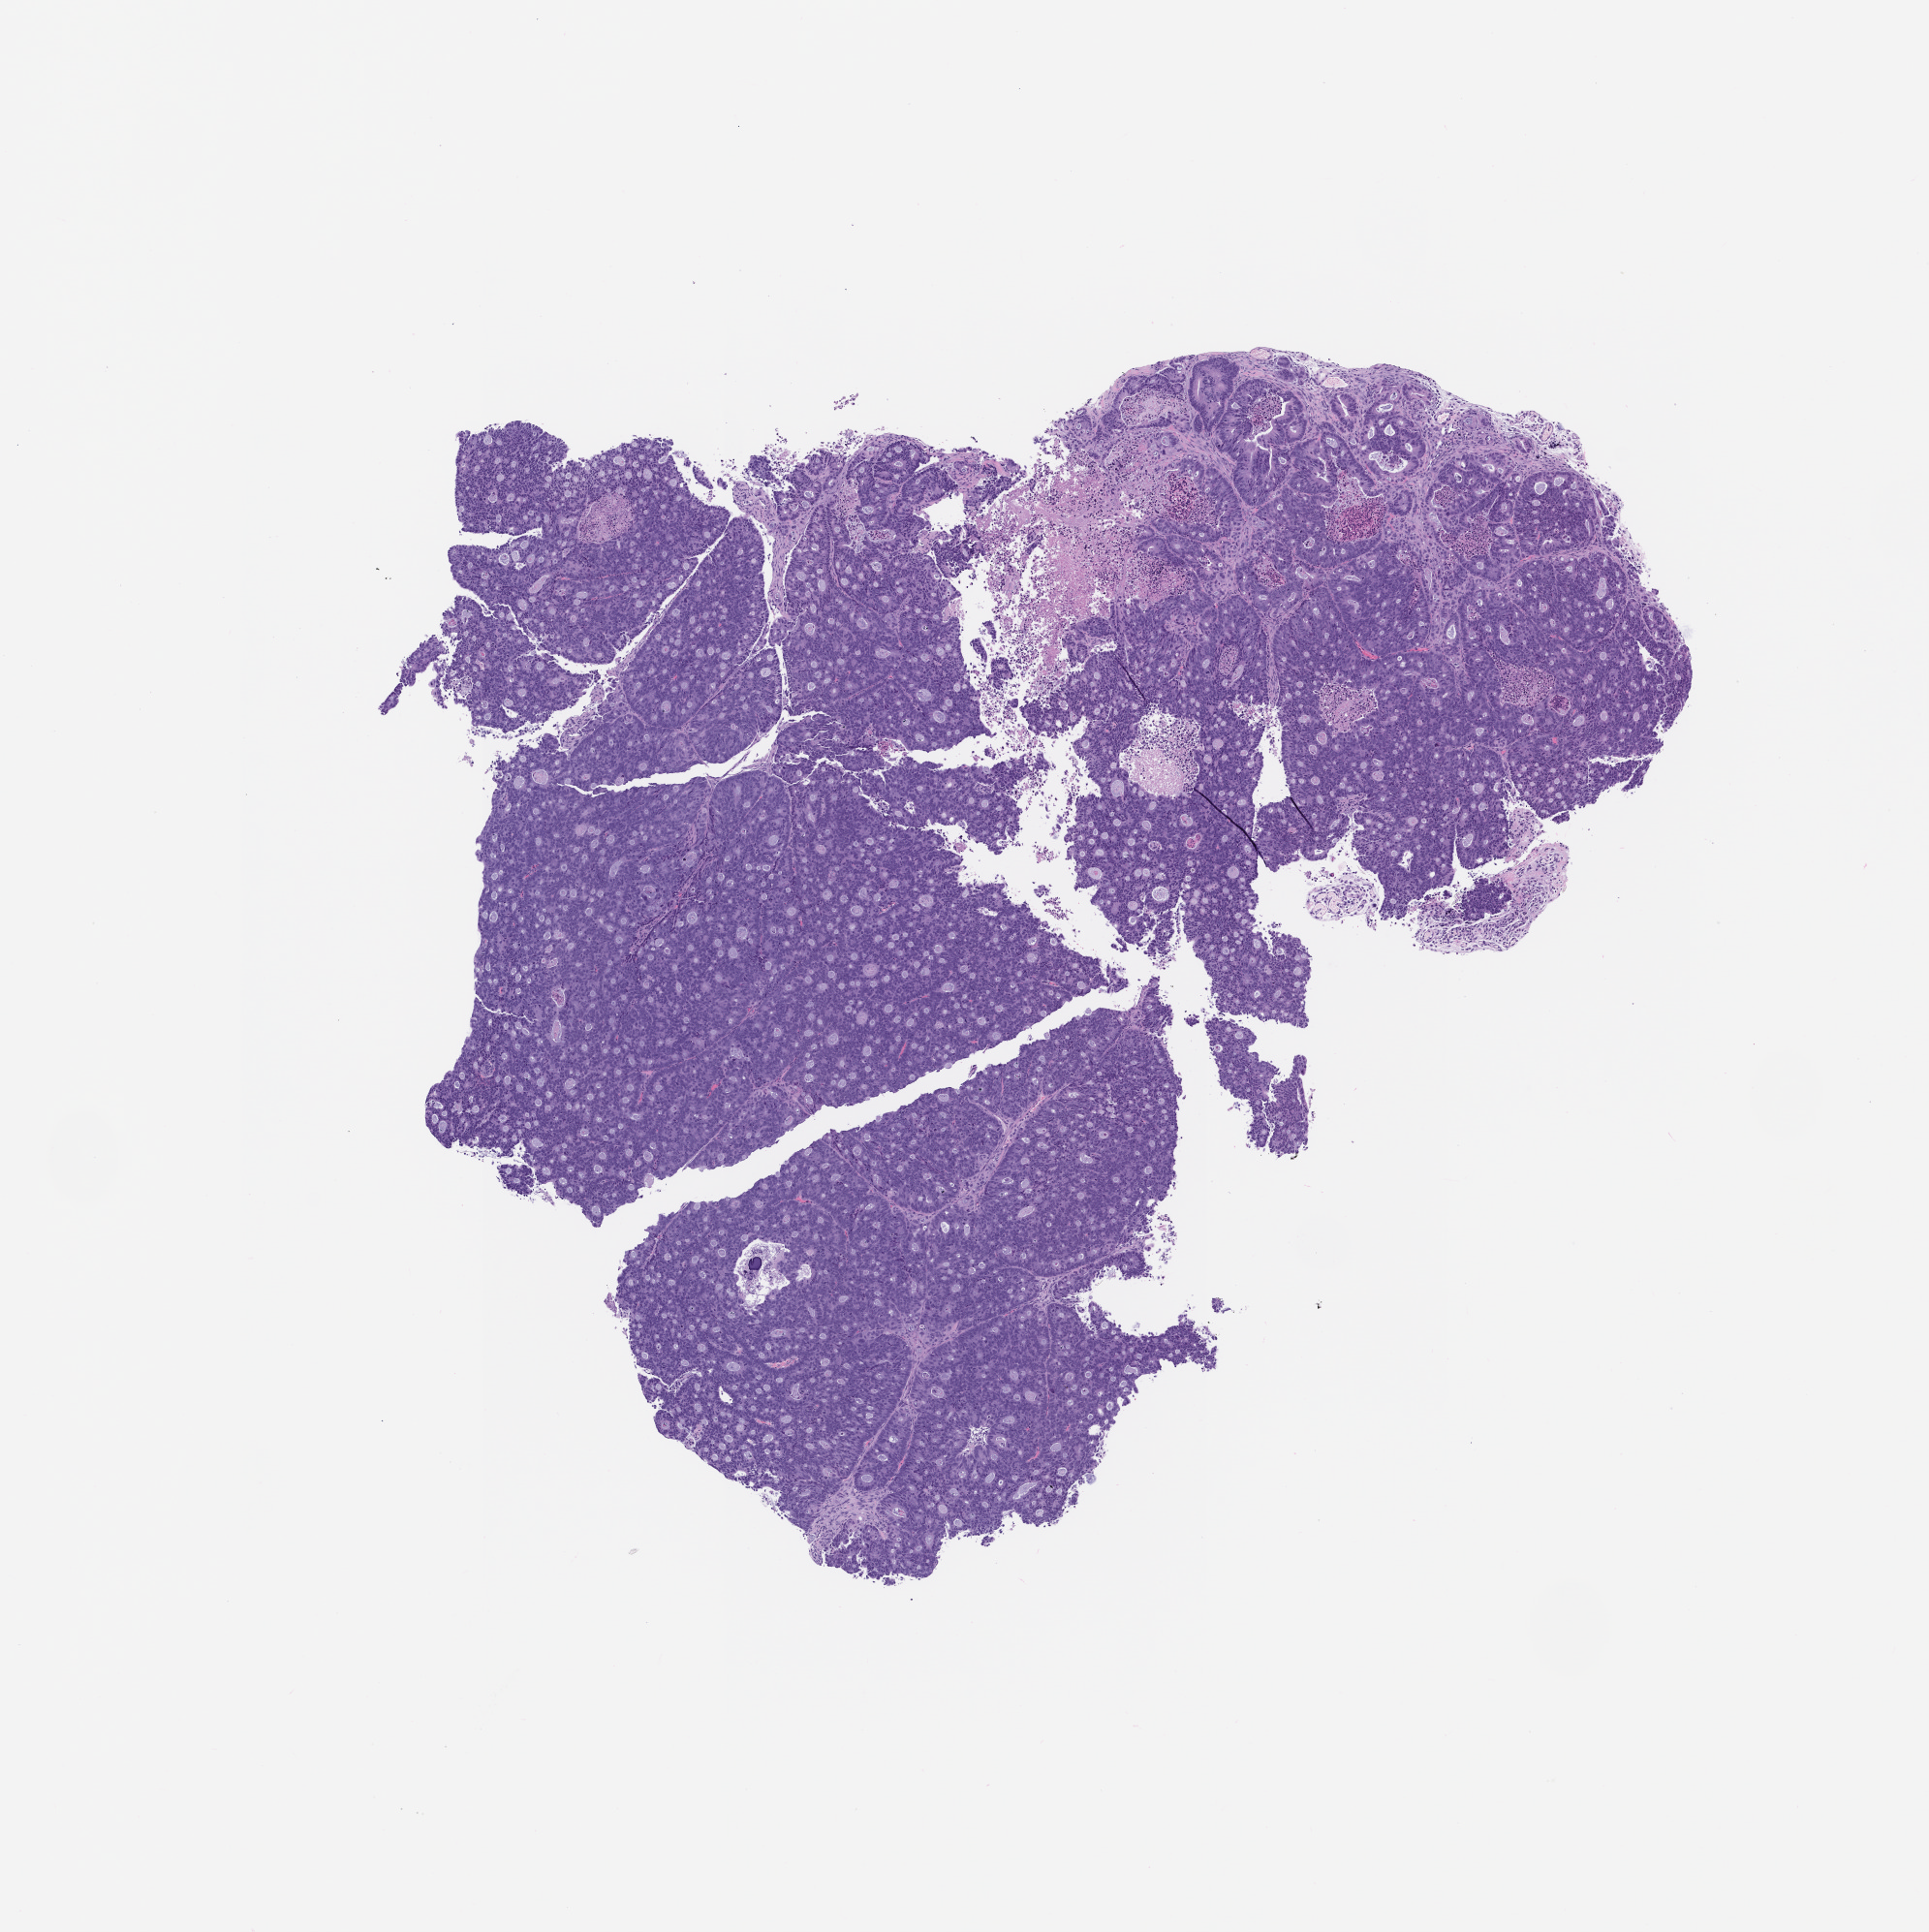
Haematoxylin and eosin whole-slide image of a patient-derived xenograft (PDX) tumor grown in a mouse, passage 2, a low-resolution overview of the entire scanned area, about 8.0 x 8.0 mm, FFPE section, tumor site category: colon.
Originating patient diagnosis: Colon Adenocarcinoma.